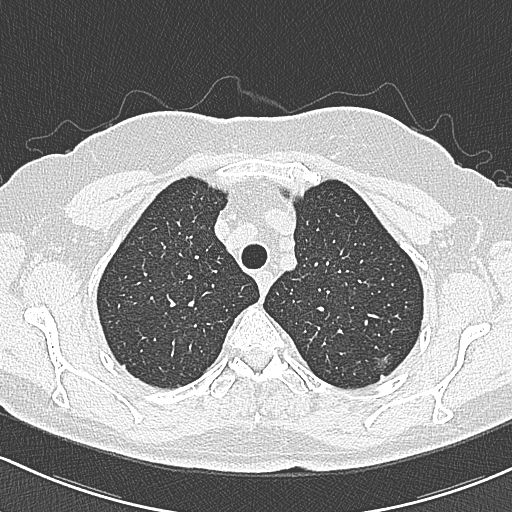
Axial slice from a low-dose chest CT screening exam, first (baseline) screen, lung window (W 1500 / L -600 HU), 1 mm slice thickness, lung (sharp) reconstruction kernel (B80f), slice 54 of 312 in the series. Female participant, aged 65 years at enrolment. Current smoker at enrolment.
- Lesion marked by an expert reader, bounding box (x1, y1, x2, y2) in pixels: (366, 342, 404, 384).
- The screening reader recorded 3 non-calcified nodules or masses ≥4 mm on this exam (left upper lobe, left upper lobe, right upper lobe); which of them this box marks is not recorded.
- Official screen result: positive, change unspecified: nodule(s) >= 4 mm or enlarging nodule(s), mass(es), or other non-specific abnormalities suspicious for lung cancer.
- Lung cancer was diagnosed 390 days after this screen: bronchiolo-alveolar carcinoma, non-mucinous, left upper lobe, stage IA (AJCC 6th edition), 10 mm at pathology.